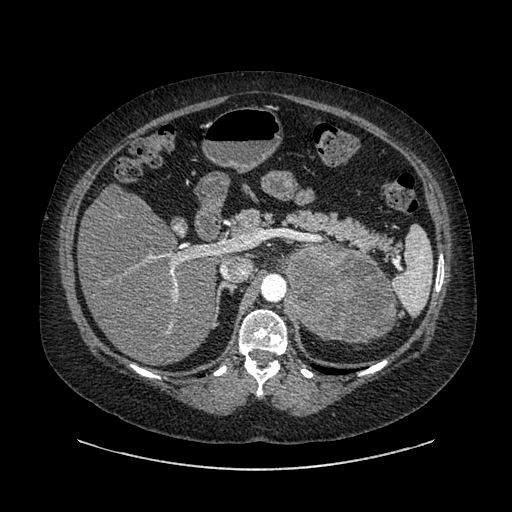
Contrast-enhanced abdominal CT, one axial slice; slice 576 of 769 in the series (ordered by position); reconstruction kernel SOFT; intravenous contrast given; soft-tissue window (W 400 / L 40 HU); 0.62 mm slice thickness; 512 × 512 image matrix. Female patient, age 61 years. Case-level facts recorded for this patient, not image findings: diagnosis: adrenocortical carcinoma; tumour side: left adrenal; tumour size at pathology: 13 cm; Ki-67 index: 79 %; stage (as recorded): 2.
Outlined on this slice (semi-automatically segmented with operator editing):
- mass: box from (x=283, y=244) to (x=393, y=343) px